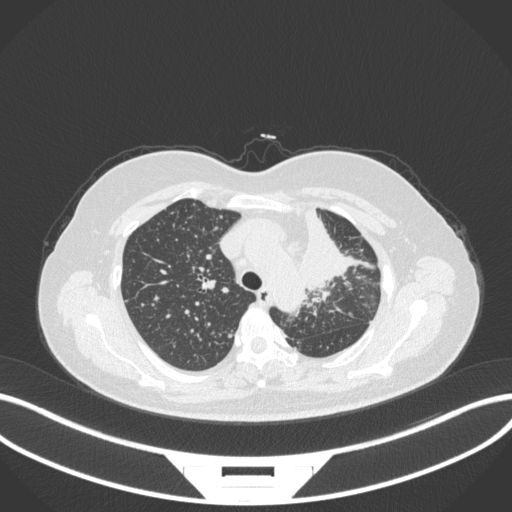
Chest CT, one axial slice. Slice 250 of 348 in the series (ordered by position). Reconstruction kernel B31f. Lung window (W 1500 / L -600 HU). 512 × 512 image matrix, field of view 400 × 400 mm. Female patient, age 49 years. Case-level facts recorded for this patient, not image findings: clinical TNM (as recorded): T1c N0 M1.
Structures marked on this image (rectangle marked by the reading radiologist):
- lung tumour (recorded histology: adenocarcinoma): bounding box <298,199,358,296> (left, top, right, bottom; pixels)